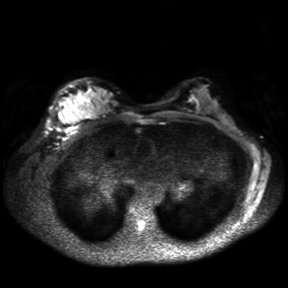
Breast MRI, one axial slice. Position 21 of 30 along the scan axis. Diffusion-weighted series; image 2 of 4 stored at this slice position (different b-values; order by instance number). 3 T. 4 mm slice thickness. 288 × 288 image matrix, field of view 360 × 360 mm. Female patient.
Structures marked on this image (manually delineated by an expert):
- tumour on diffusion-weighted imaging: bounding box <59,102,69,123> (left, top, right, bottom; pixels)